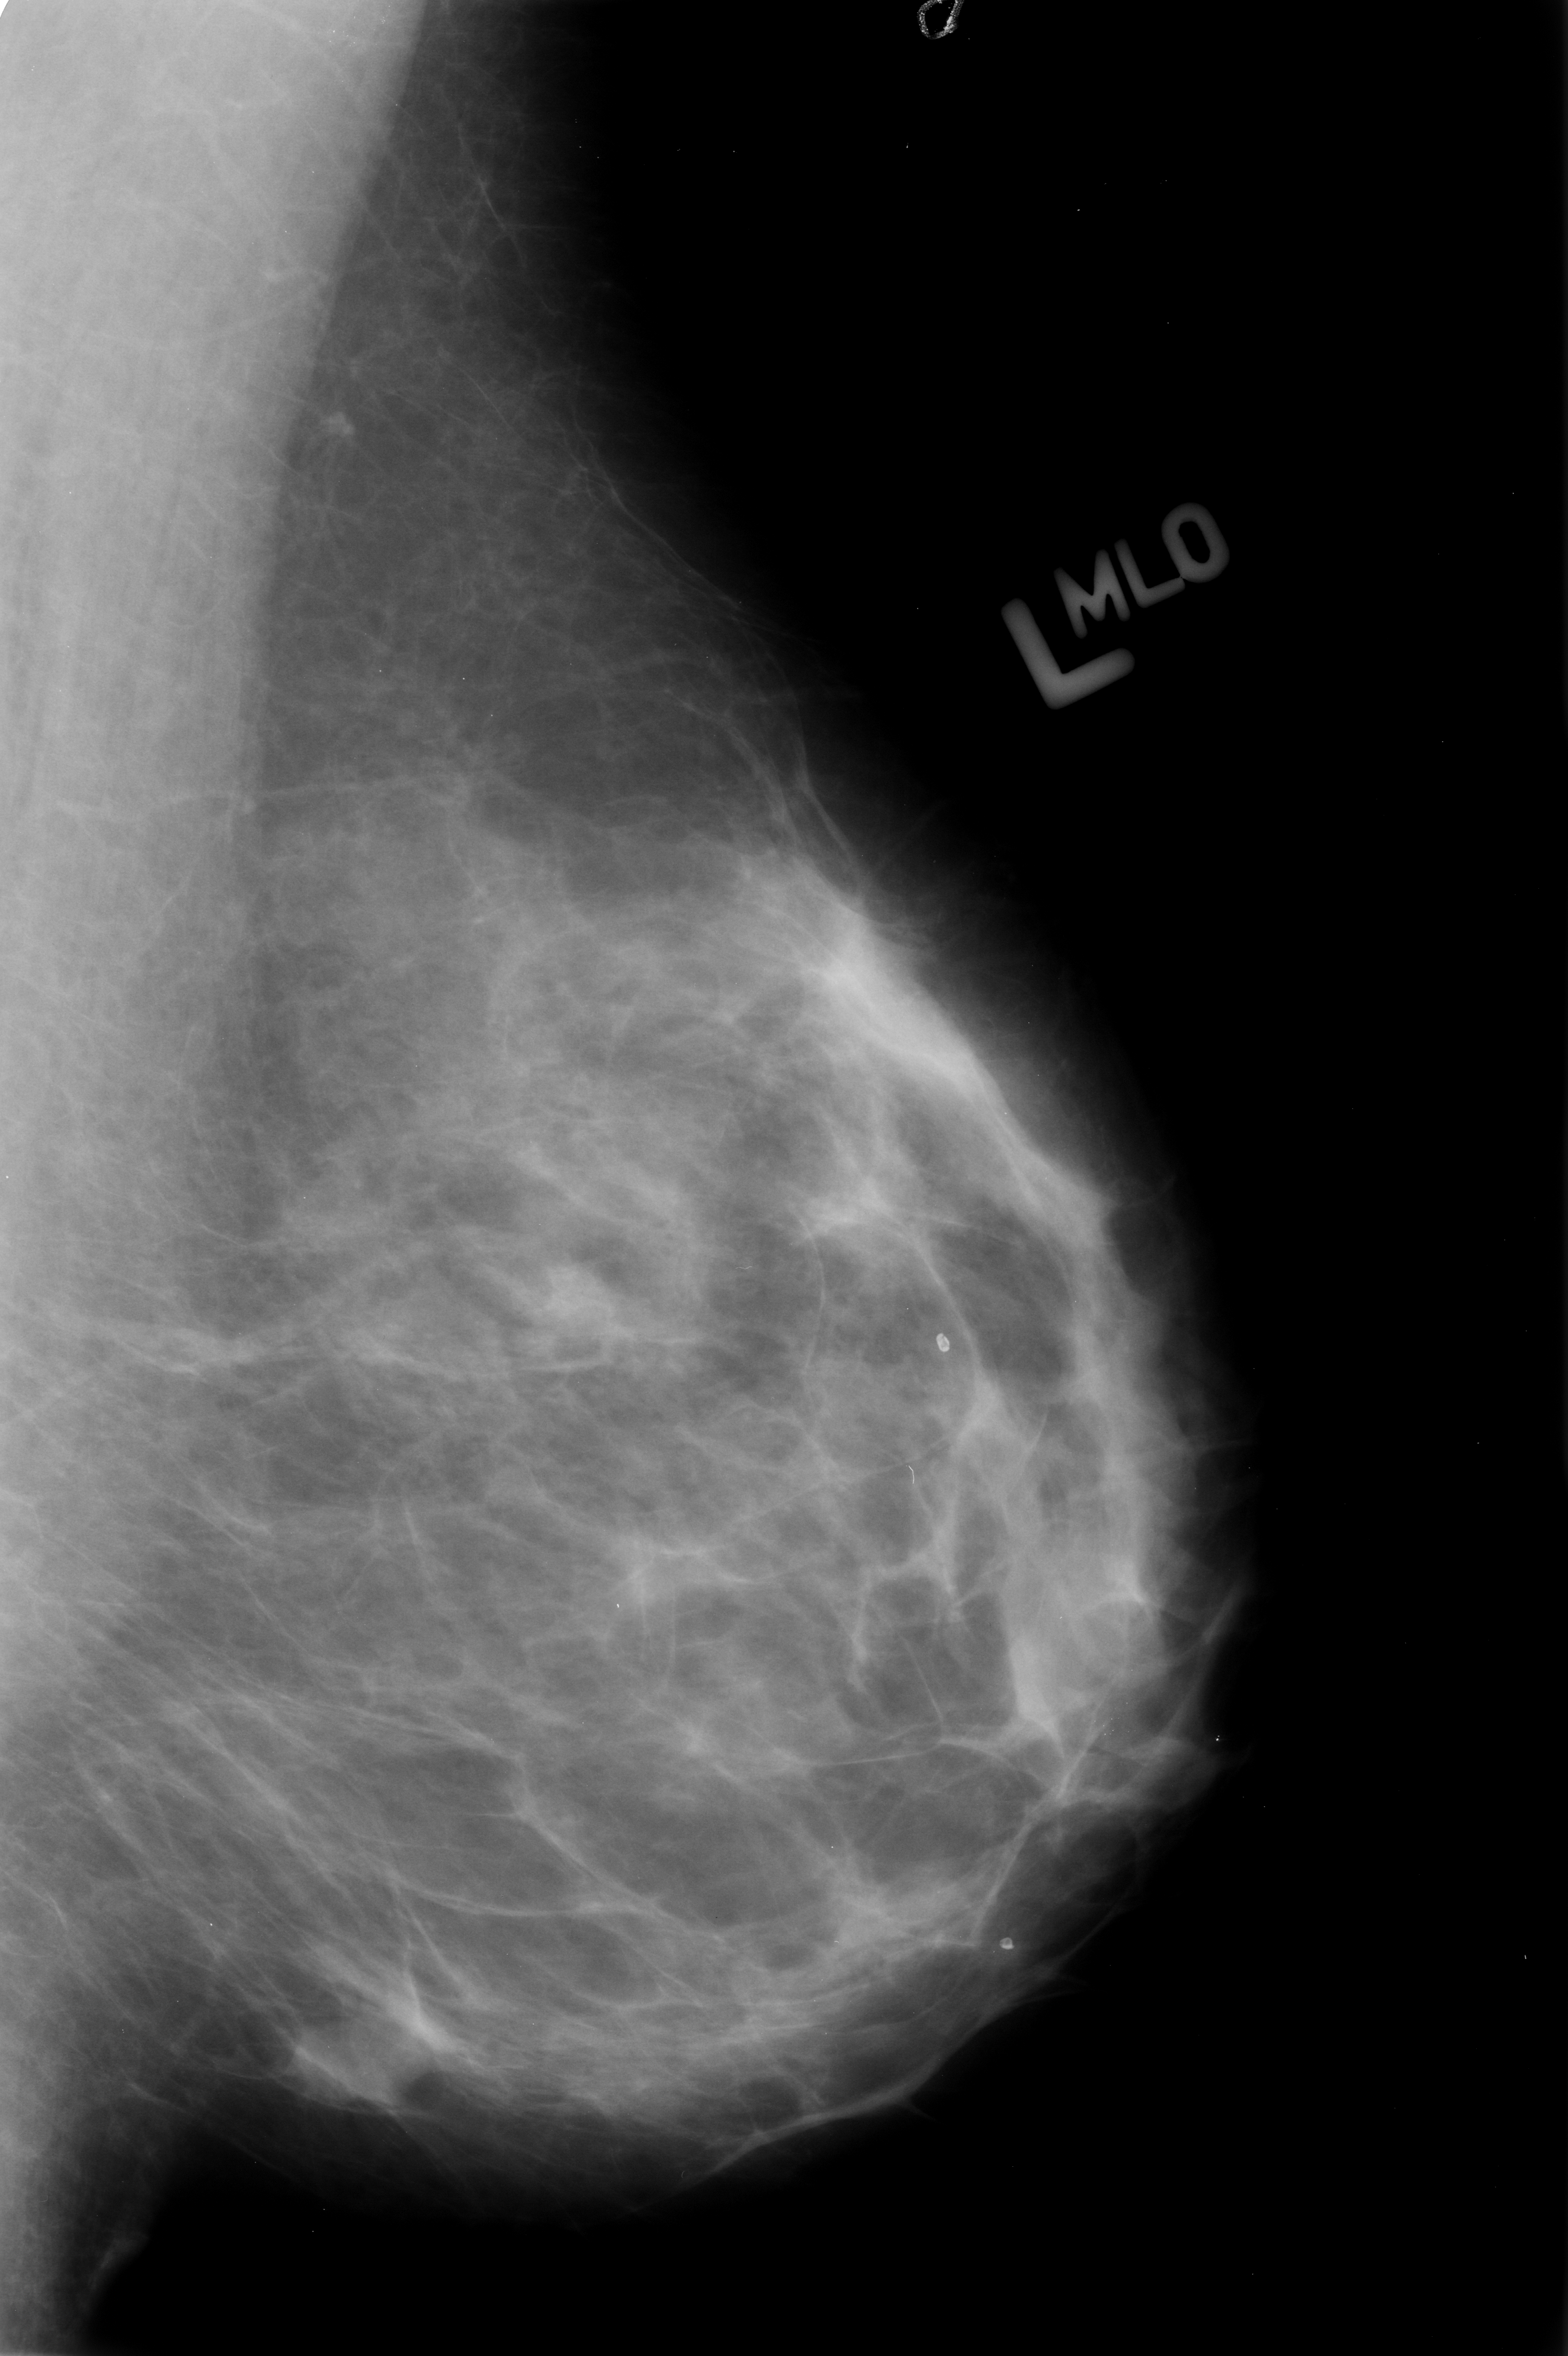
Digitized screen-film mammogram. Left breast. Mediolateral oblique (MLO) view. 1568 × 2356 image matrix.
Expert-marked regions of interest on this image (one box per marked abnormality):
- mass, shape irregular, margins ill defined; BI-RADS assessment category 4; subtlety rating 3 on a 1 (subtle) to 5 (obvious) scale; pathology (as recorded): malignant: box from (x=249, y=1988) to (x=453, y=2139) px